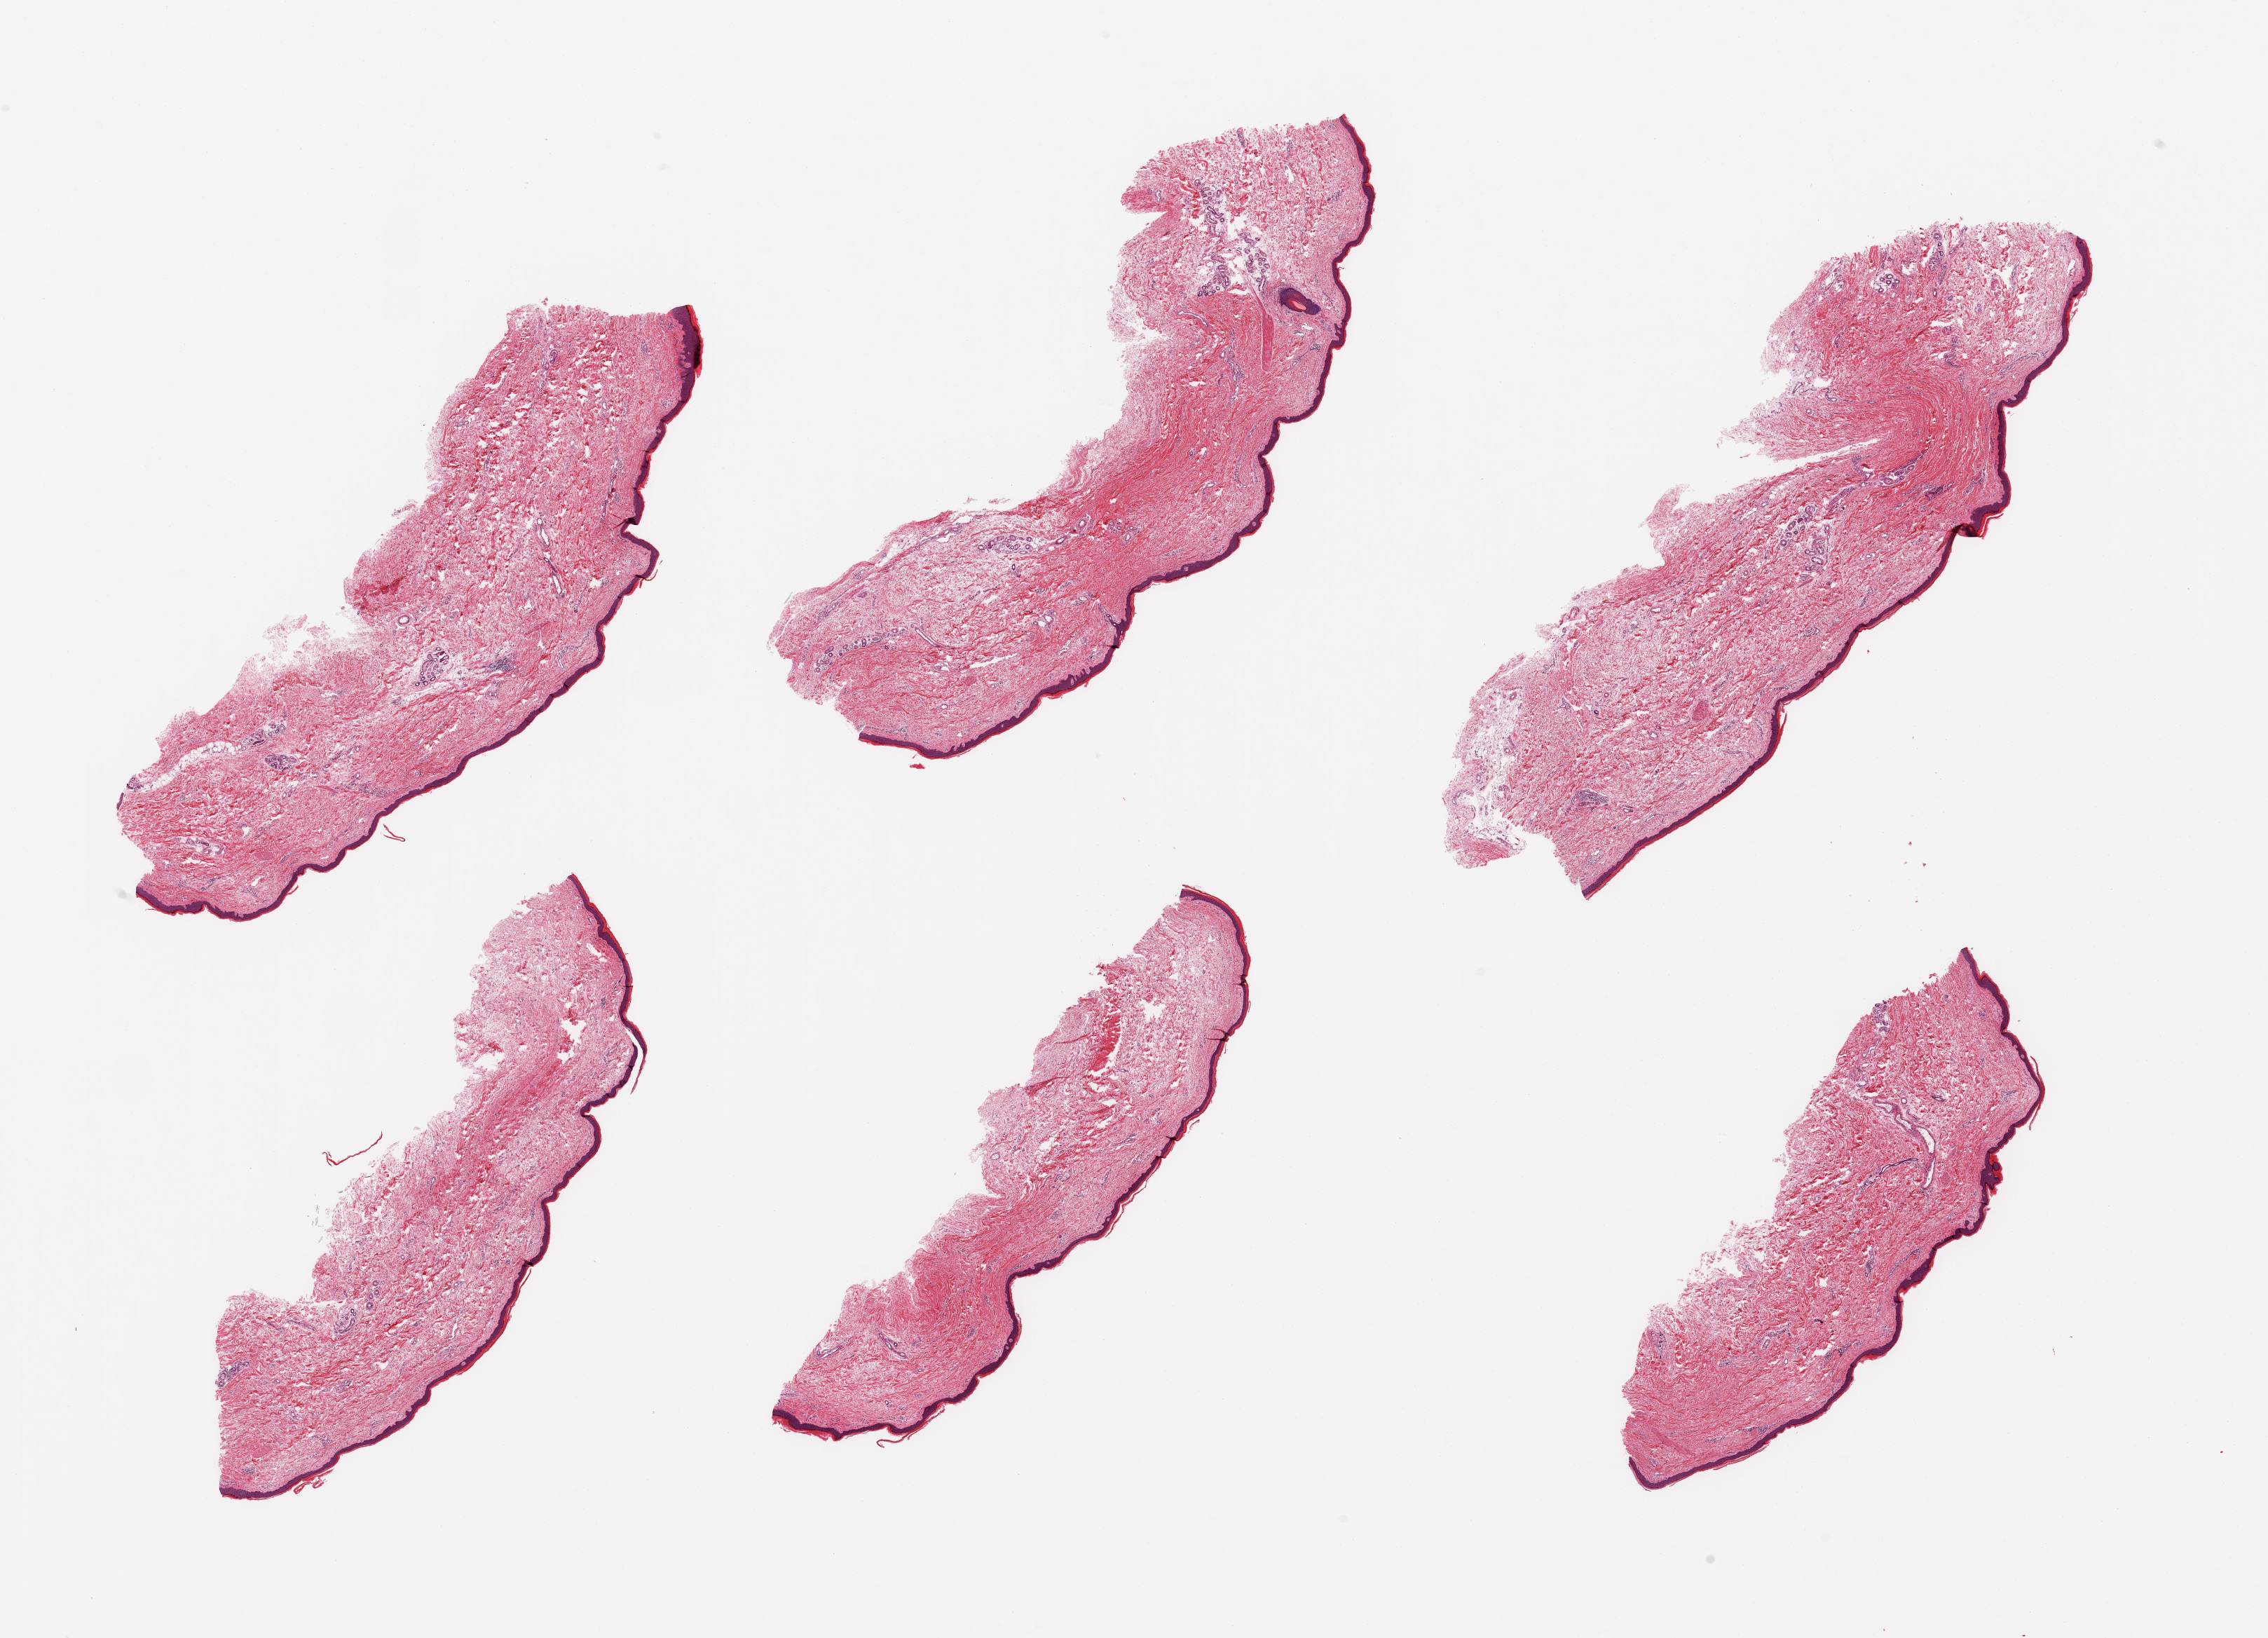
Whole-slide image, H&E stain, shown as a low-resolution overview of the whole scanned area (about 25.6 x 18.5 mm), PAXgene-fixed, paraffin-embedded tissue, target tissue: skin of lower leg, donor tissue sample. Male donor.
Reviewer comment on this tissue sample: 6 pieces; no significant dermal fat; squamous epithelium is ~50 microns.